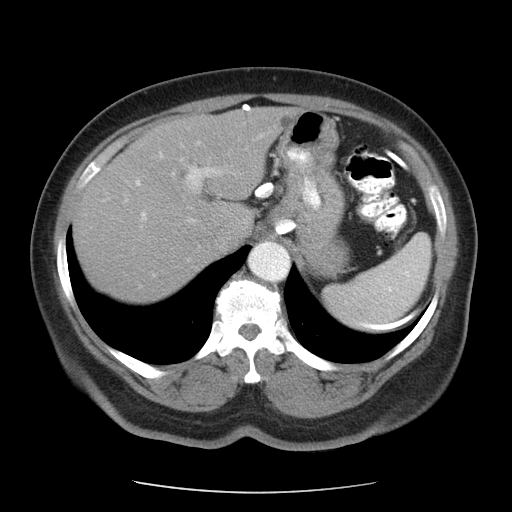
Contrast-enhanced abdominal CT, one axial slice; slice 75 of 95 in the series (ordered by position); reconstruction kernel STANDARD; 120 kVp; intravenous contrast given; soft-tissue window (W 400 / L 40 HU); 5 mm slice thickness; 512 × 512 image matrix, field of view 362 × 362 mm. Patient: female, 71 years. Case-level facts recorded for this patient, not image findings: diagnosis: adrenocortical carcinoma; tumour side: left adrenal; tumour size at pathology: 8.8 cm; Ki-67 index: 20 %; stage (as recorded): 2.
Annotated regions visible in this slice (semi-automatically segmented with operator editing):
- mass: bounding box [x1, y1, x2, y2] px = [307, 238, 348, 276]